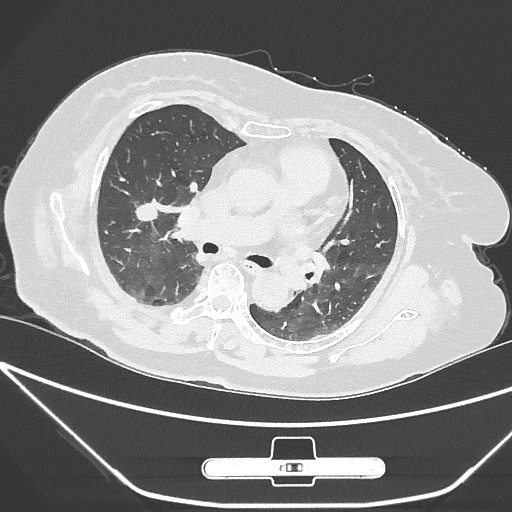
Chest CT, one axial slice. Slice 157 of 245 in the series (ordered by position). Reconstruction kernel IMR1,SharpPlus. 120 kVp. Lung window (W 1500 / L -600 HU). 1 mm slice thickness. 512 × 512 image matrix. Female patient, age 65 years. Case-level facts recorded for this patient, not image findings: clinical TNM (as recorded): T1c N0 M0.
Annotated regions visible in this slice (bounding box drawn by a radiologist):
- lung tumour (recorded histology: adenocarcinoma): bounding box [x1, y1, x2, y2] px = [132, 192, 163, 232]